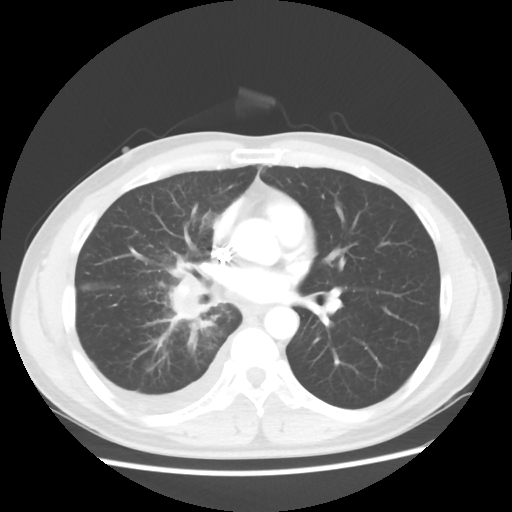
Chest CT, one axial slice. Slice 27 of 56 in the series (ordered by position). Reconstruction kernel STANDARD. Lung window (W 1500 / L -600 HU). 5 mm slice thickness. 512 × 512 image matrix. Patient: male, 46 years. From the clinical record (not read from this slice): clinical TNM (as recorded): T2 N3 M1.
Structures marked on this image (rectangle marked by the reading radiologist):
- lung tumour (recorded histology: adenocarcinoma): bounding box <166,268,213,333> (left, top, right, bottom; pixels)